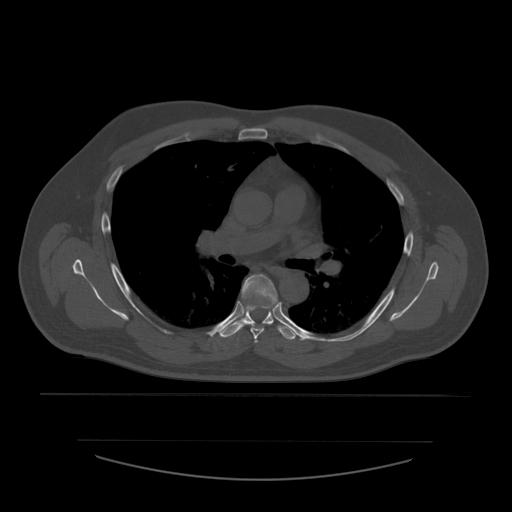
CT including the spine, one axial slice. Position 388 of 532 along the scan axis. Reconstruction kernel STANDARD. 120 kVp. Bone window (W 1800 / L 400 HU). 1.25 mm slice thickness. 512 × 512 image matrix, field of view 441 × 441 mm. Patient age 44 years. Case-level facts recorded for this patient, not image findings: primary cancer: soft tissue sarcoma.
Annotated regions visible in this slice (semi-automatic segmentation, software-assisted and operator-edited):
- T4 vertebra: bounding box [x1, y1, x2, y2] px = [255, 339, 258, 343]
- T5 vertebra: [242, 274, 278, 340]
- T6 vertebra: [220, 300, 298, 340]